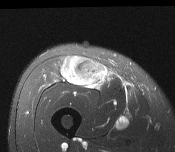
MRI of an extremity soft-tissue mass, one axial slice; slice 64 of 116 in the series (ordered by position); T2-weighted fat-saturated; MR volume resampled by the dataset authors to the PET/CT grid (not the native acquisition matrix); 3.27 mm slice thickness; 175 × 152 image matrix, field of view 171 × 148 mm. Male patient. Case-level facts recorded for this patient, not image findings: histological type: pleiomorphic leiomyosarcoma; grade: intermediate; site of the primary tumour: right thigh.
Annotated regions visible in this slice (expert contour drawn on MRI and transferred to this co-registered scan by the dataset authors):
- gross tumour volume including surrounding oedema: bounding box <61,56,107,87> (left, top, right, bottom; pixels)